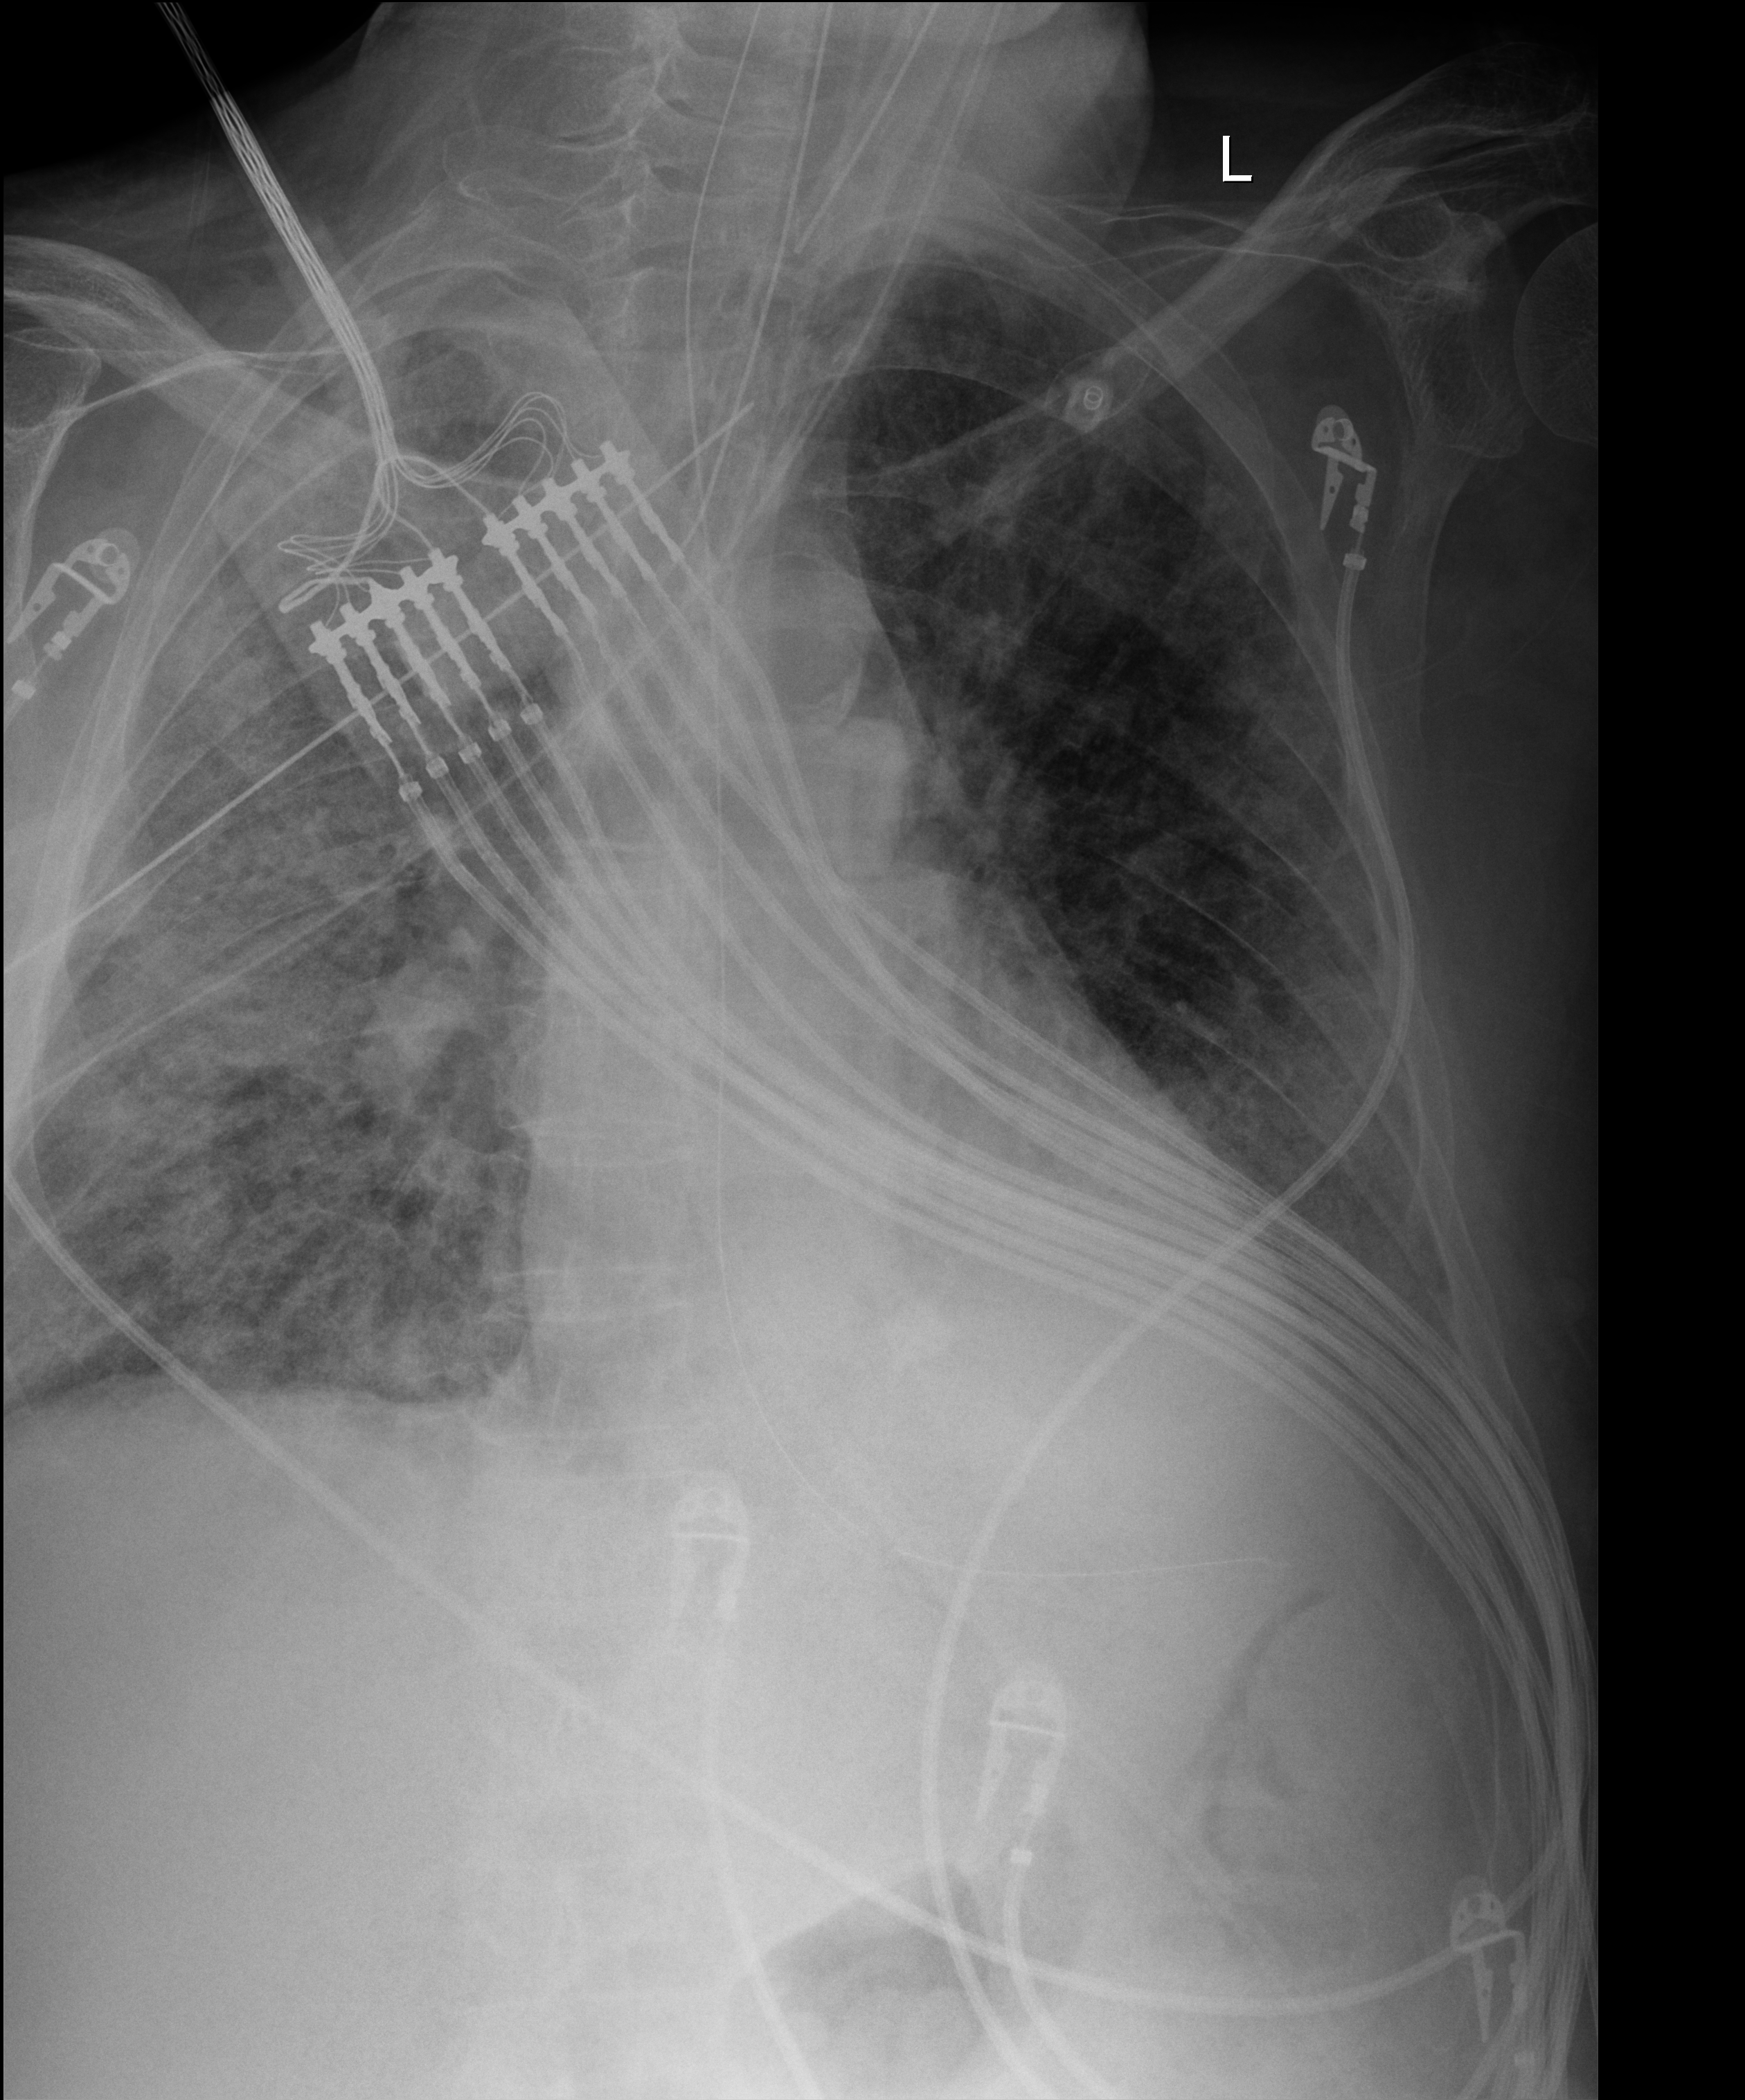
Chest X-ray (portable), anteroposterior (AP) projection. Patient hospitalised with COVID-19; male, aged 60–74 years.
Hospital-stay facts (about this admission, not read from this image; timing relative to this image not recorded): hypertension (admission record): no; chronic kidney disease (admission record): no.